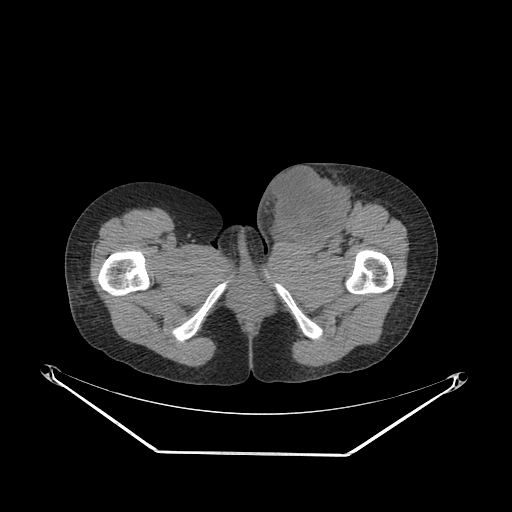
CT of an extremity soft-tissue mass (from a PET/CT study), one axial slice. Position 54 of 267 along the scan axis. 140 kVp. Soft-tissue window (W 400 / L 40 HU). 512 × 512 image matrix, field of view 500 × 500 mm. Female patient. Case-level facts recorded for this patient, not image findings: histological type: leiomyosarcoma; grade: high; site of the primary tumour: groin.
Annotated regions visible in this slice (expert contour drawn on MRI and transferred to this co-registered scan by the dataset authors):
- gross tumour volume including surrounding oedema: bounding box <253,162,368,245> (left, top, right, bottom; pixels)
- gross tumour volume (mass): <267,167,348,243>